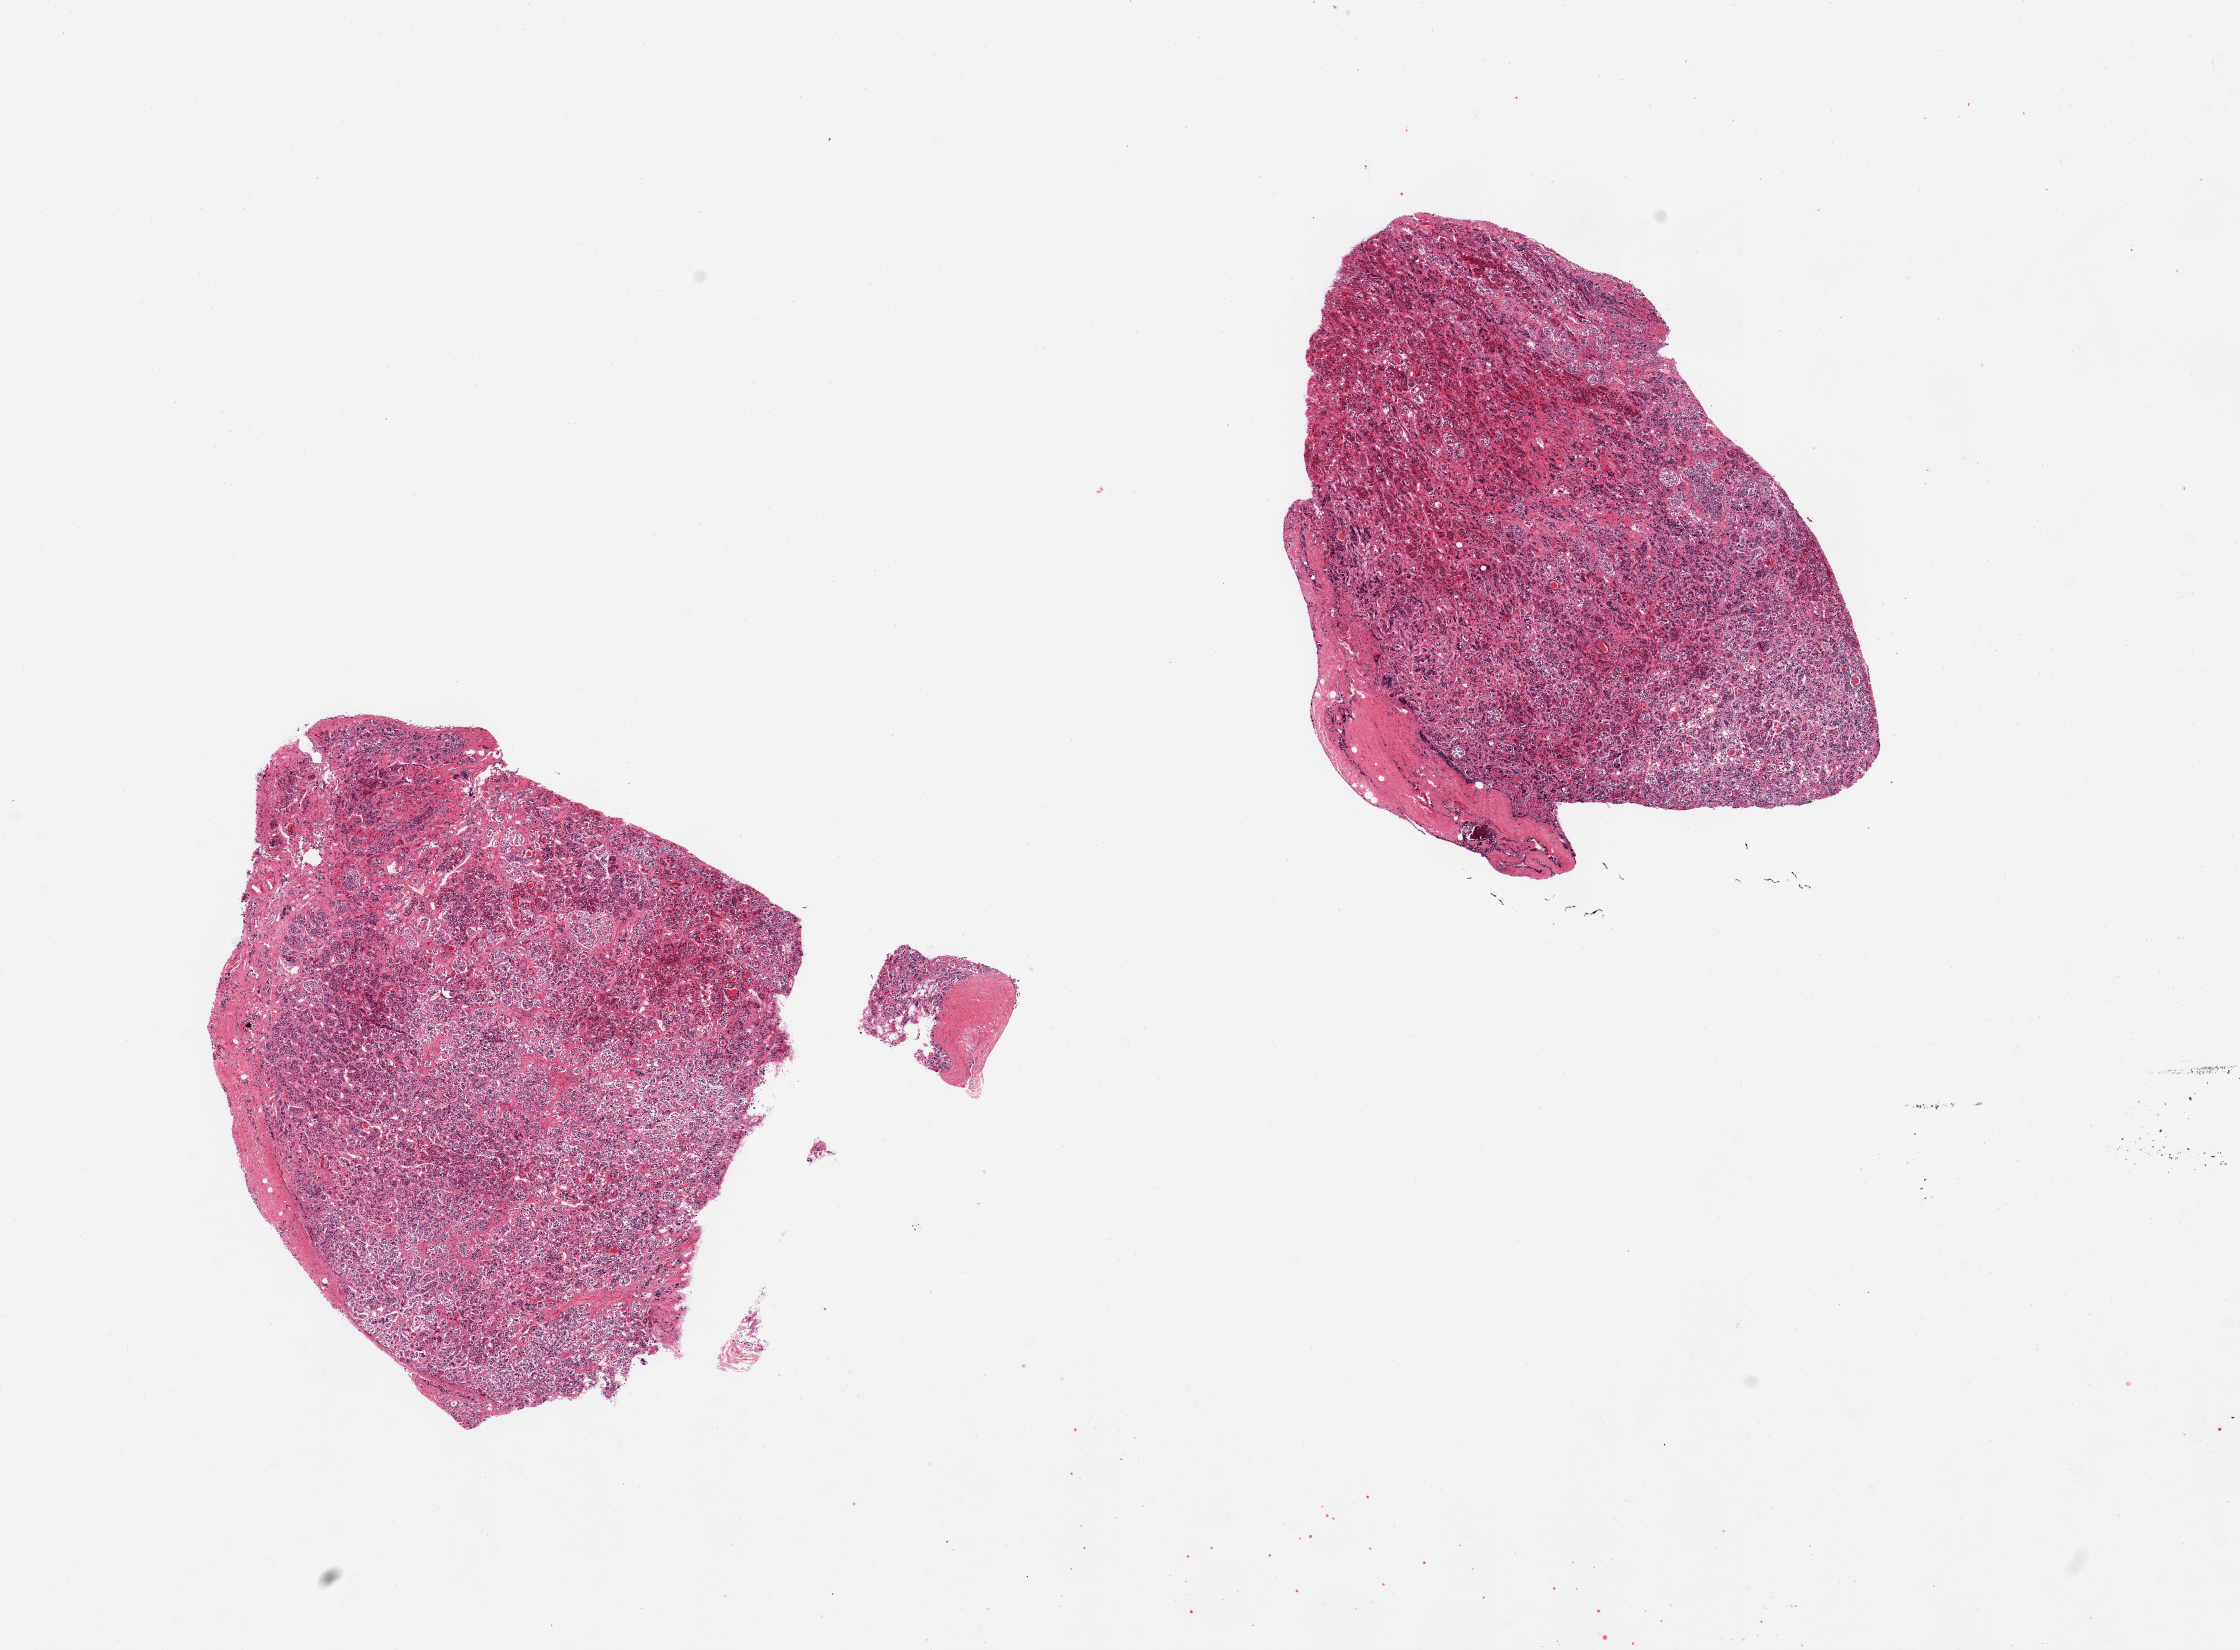
Haematoxylin and eosin whole-slide image — whole scanned area (about 17.7 x 13.1 mm, slide scanned at 20x) shown as a low-resolution overview; PAXgene-fixed paraffin-embedded (PFPE) section; section of pituitary (target tissue); tissue donor sample.
Pathologist's review note for this sample: 2 pieces, adenohypophysis.